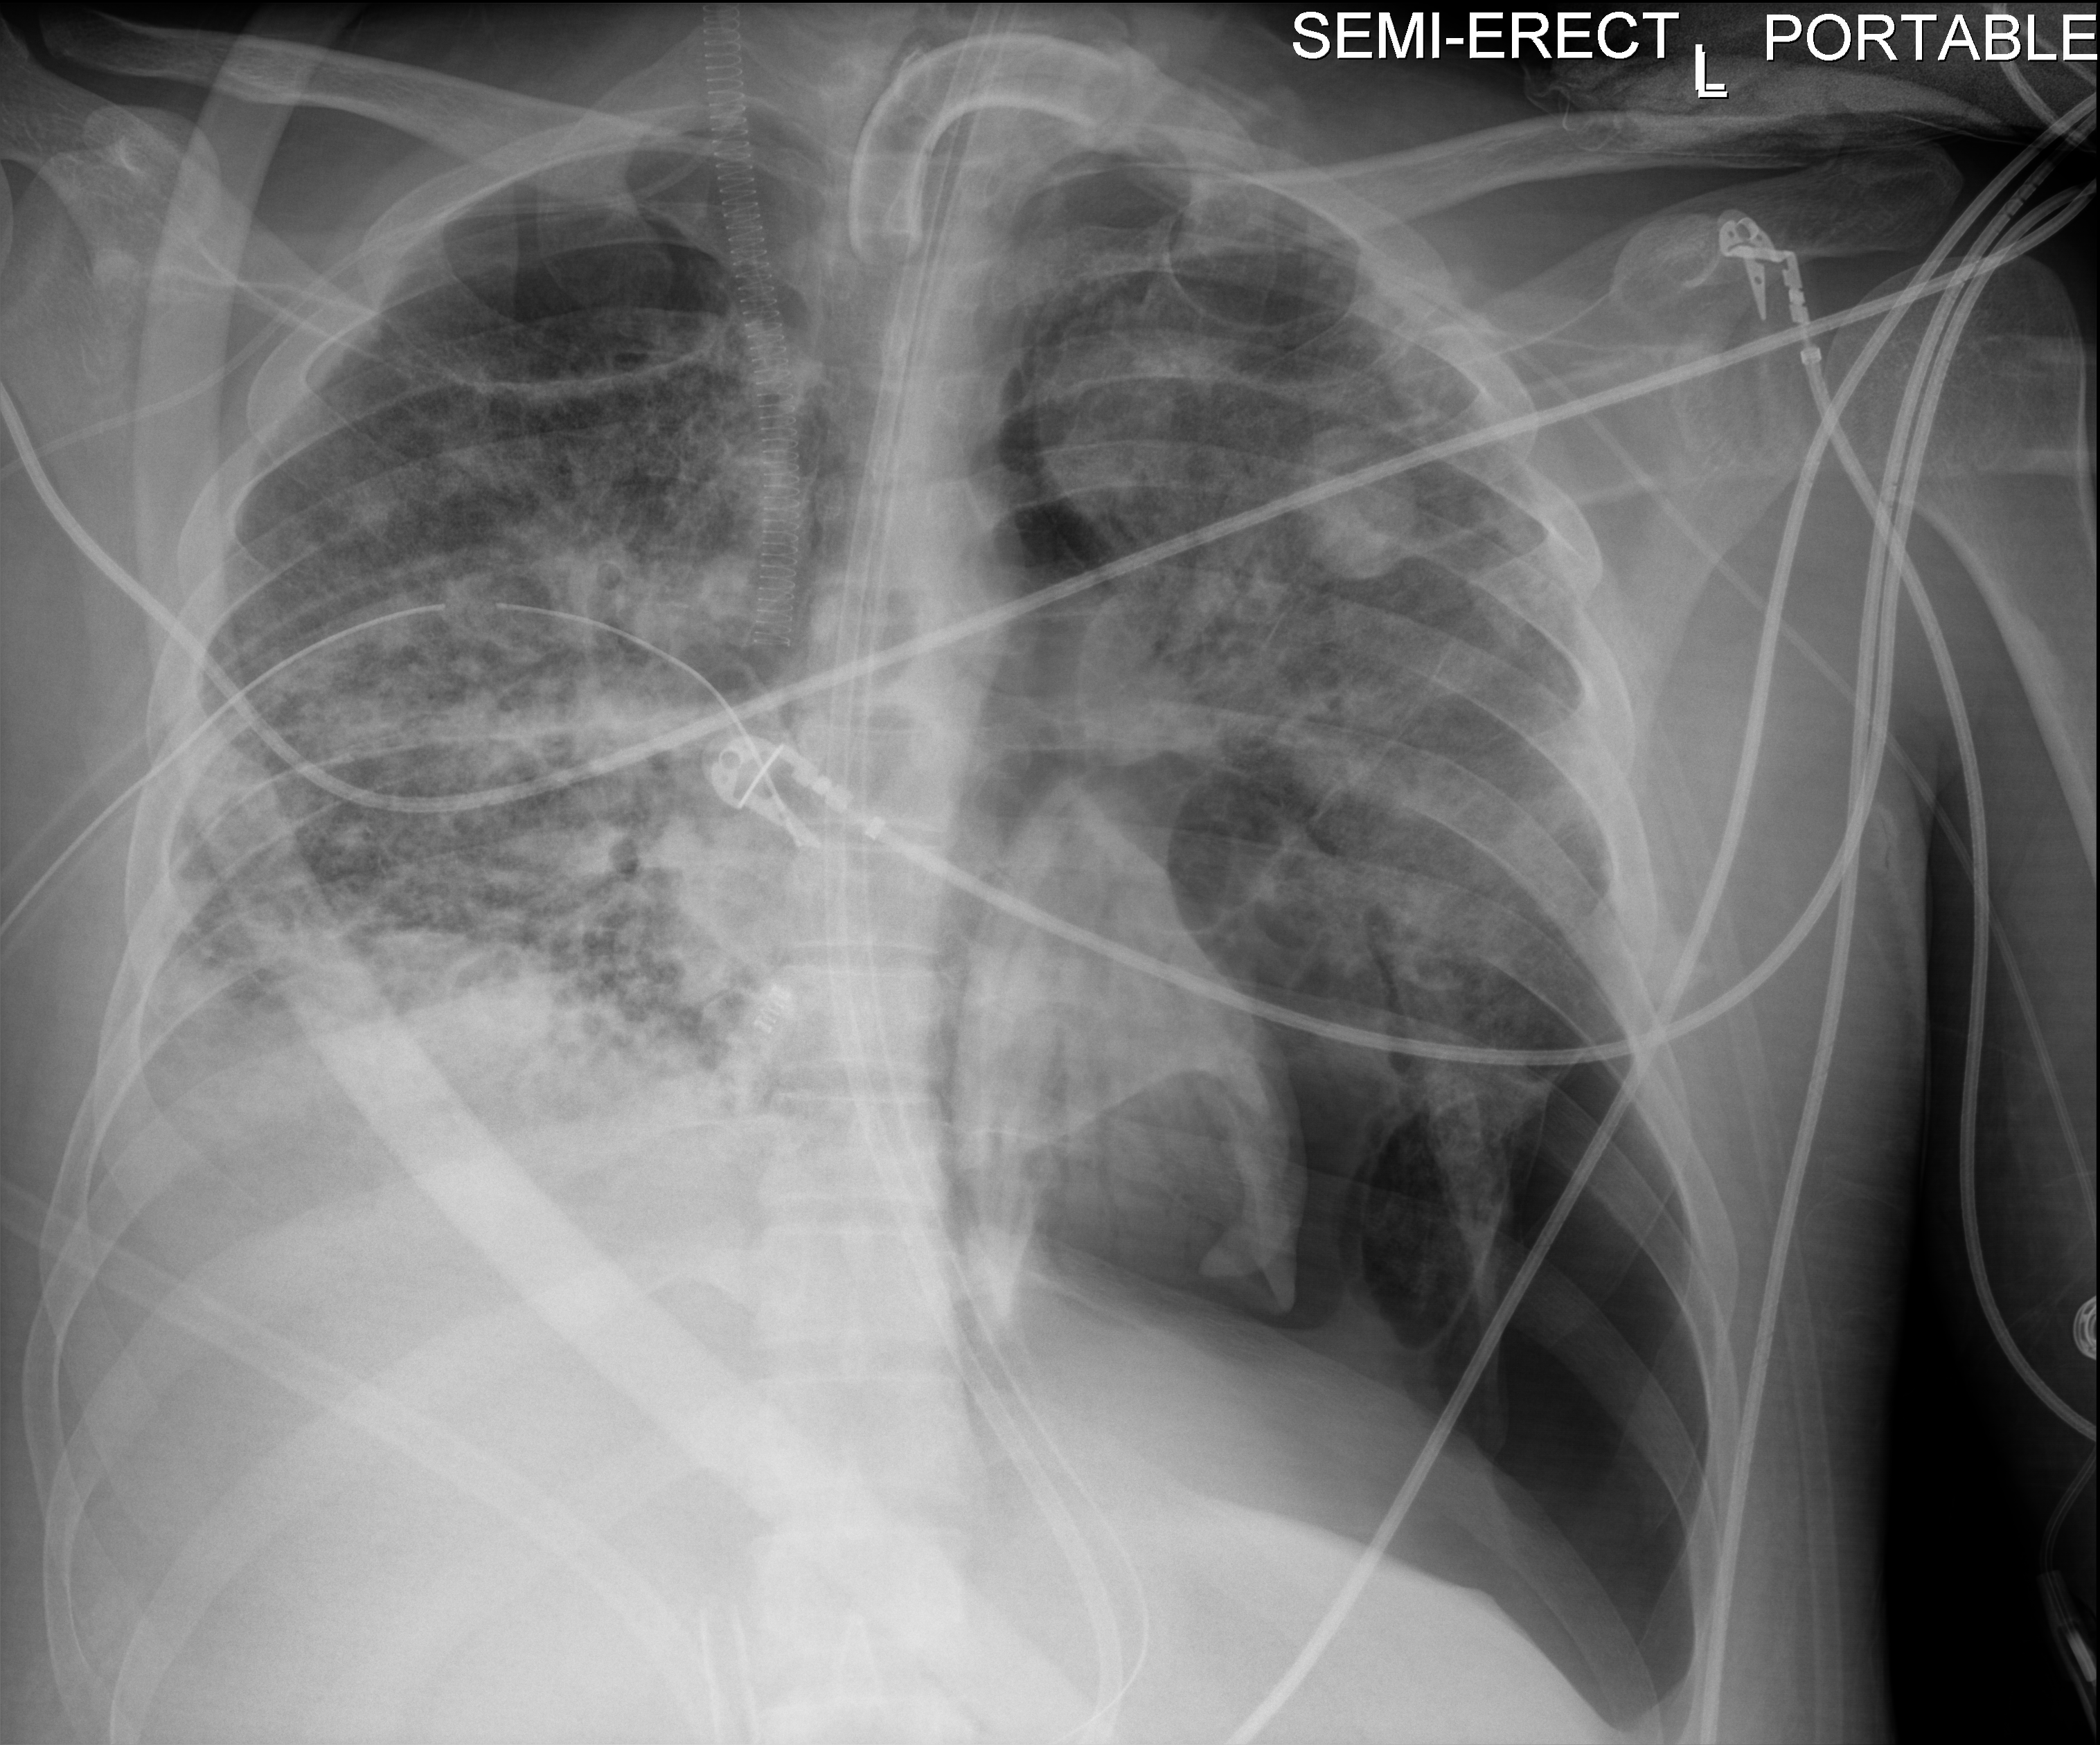
Bedside chest radiograph (digital radiography), anteroposterior (AP) projection. Patient hospitalised with COVID-19, aged 18–59 years.
From the hospital-stay record, not from the radiograph (when in the stay this image was taken is not recorded): COPD (admission record): no; length of hospital stay: 60 days.